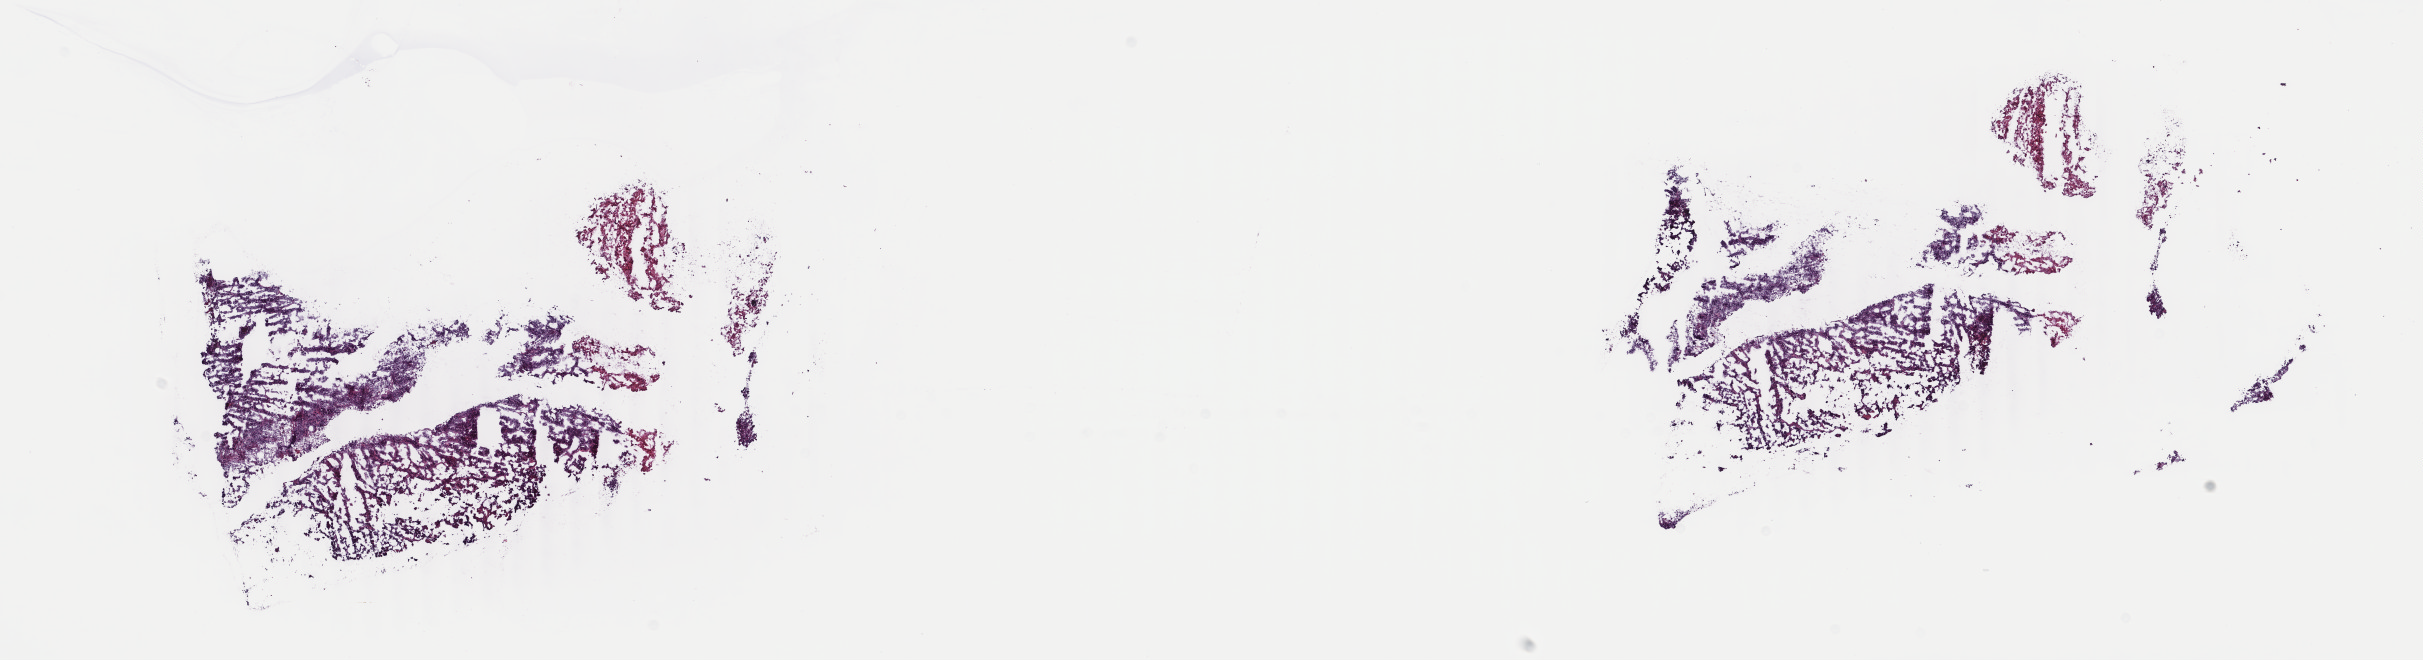
Hematoxylin and eosin (H&E) stained whole-slide image — low-resolution overview of the scanned area, about 19.3 x 5.3 mm. Frozen section from the top of the tissue portion. Primary tumour sample from the adrenal cortex. Male, age 14 years at initial diagnosis. Slide review estimates, as recorded: tumour cells 90%, tumour nuclei 90%, normal cells 0%, stromal cells 0%, necrosis 10%. Infiltration values recorded for this section: lymphocyte infiltration 40%, monocyte infiltration 20%, neutrophil infiltration 20%.
Histologic diagnosis: Adrenal cortical carcinoma (cortex of adrenal gland). Laterality: left.